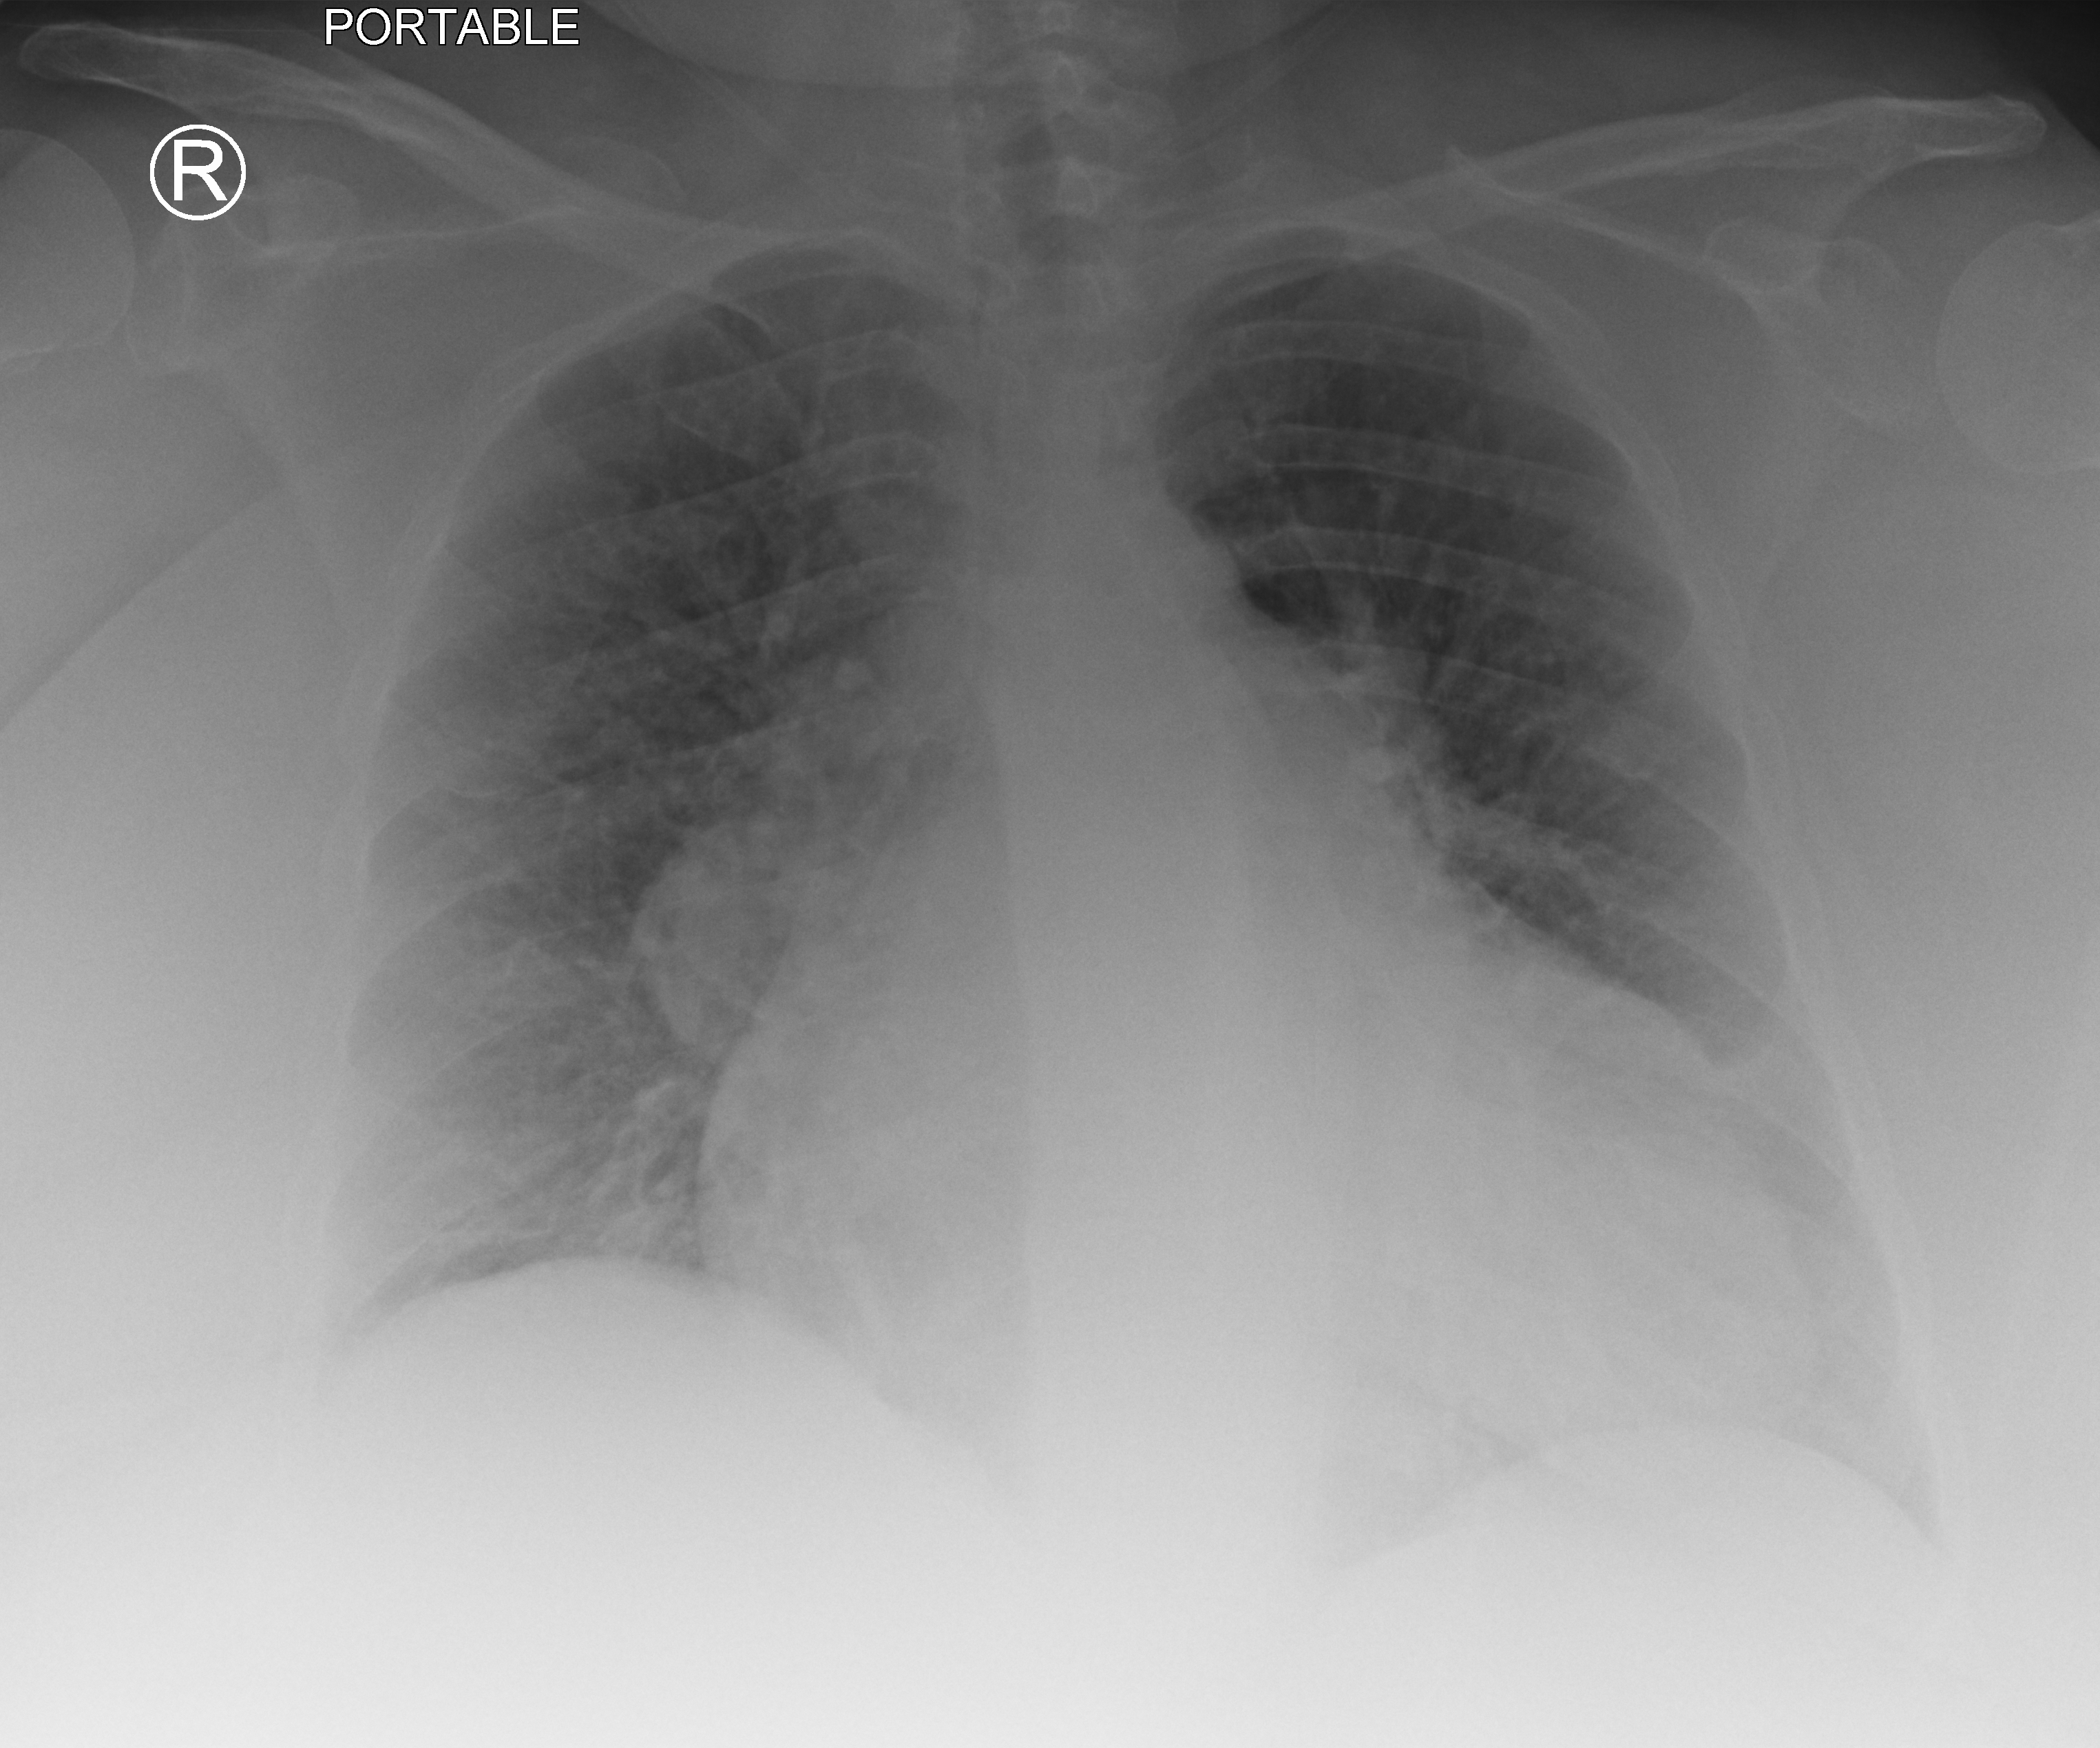
Chest X-ray (portable). Patient hospitalised with COVID-19; female, aged 60–74 years.
From the hospital-stay record, not from the radiograph (when in the stay this image was taken is not recorded): COPD (admission record): yes.